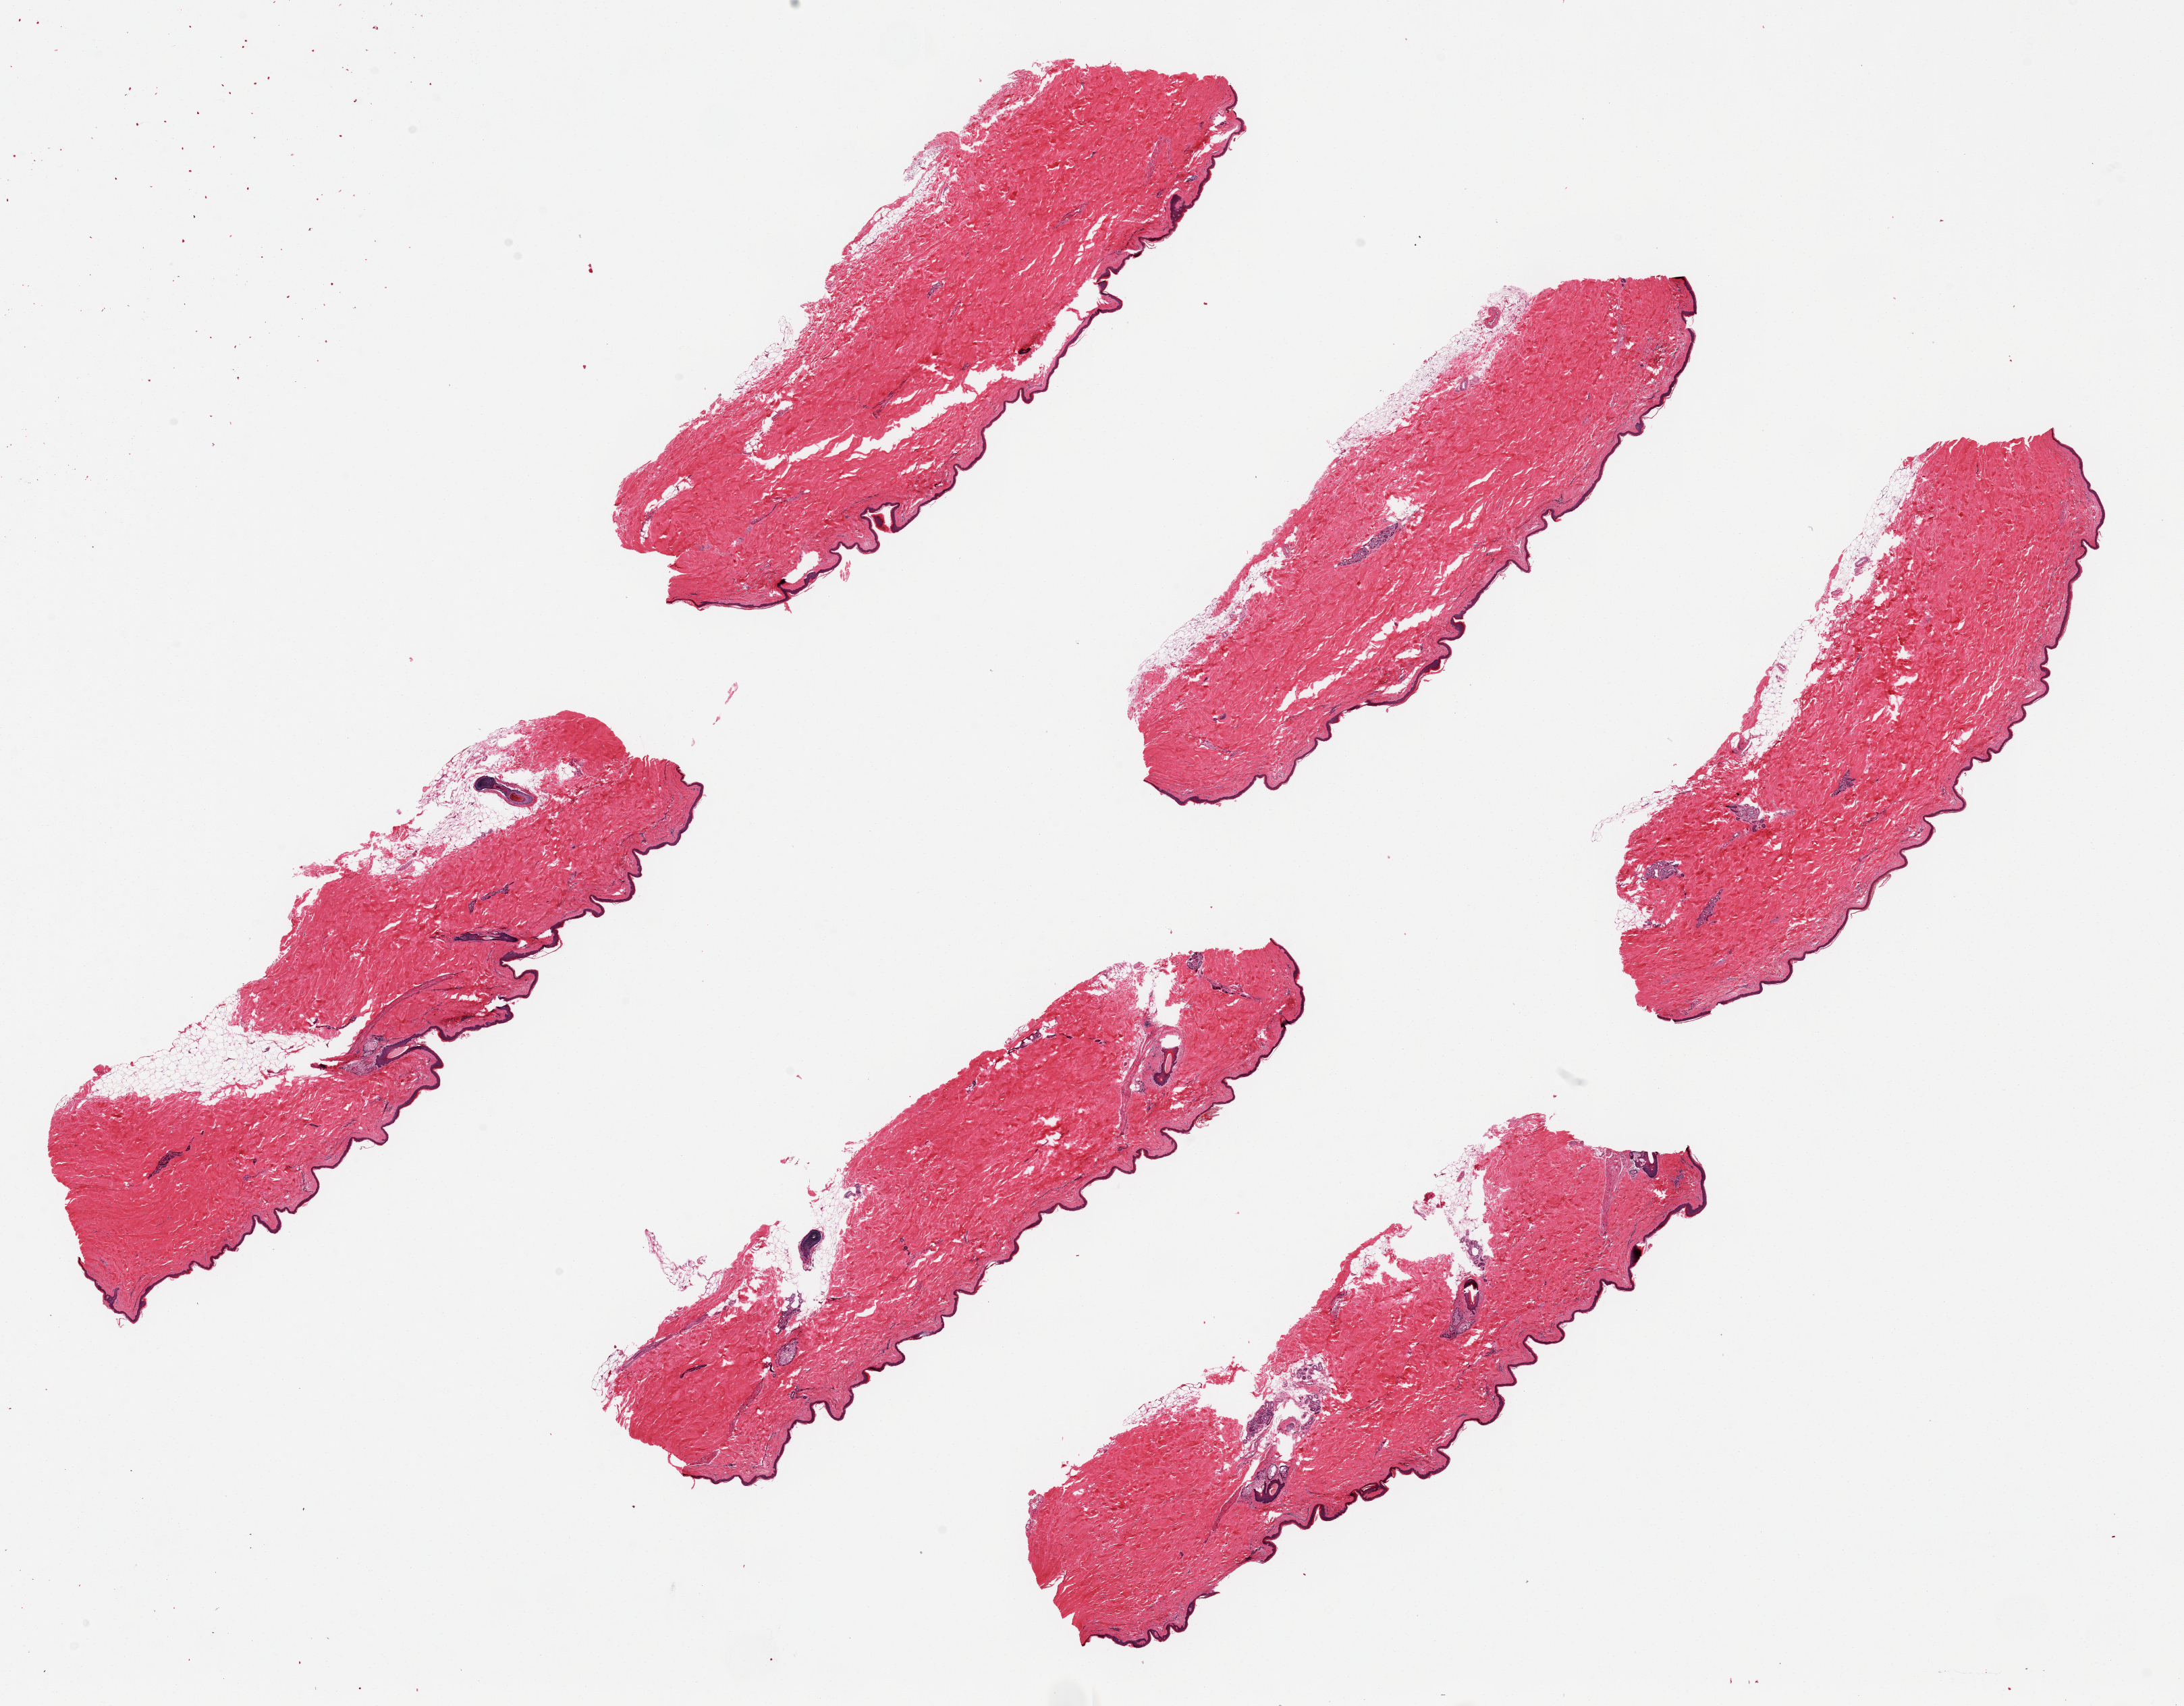
Whole-slide image, H&E stain, brightfield — low-resolution overview of the scanned area, about 25.6 x 20.0 mm, PAXgene-fixed, paraffin-embedded tissue, target tissue: skin of lower leg, donor tissue sample. Male donor.
Reviewer comment on this tissue sample: 6 ~8.5x3mm pieces; squamous epithelium is ~1-2% of thickness.